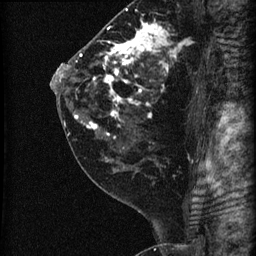
Breast MRI (dynamic contrast-enhanced), one sagittal slice. Position 38 of 60 along the scan axis. Dynamic contrast-enhanced series, image 2 of 3 at this slice position (ordered by acquisition). 1.5 T. TE 4.2 ms, TR 22.7 ms. 1.8 mm slice thickness. 256 × 256 image matrix. Patient: female, 45 years. Case-level facts recorded for this patient, not image findings: setting: breast cancer imaged before/during neoadjuvant chemotherapy; receptor status: HR-positive, HER2-negative.
Annotated regions visible in this slice (semi-automatically segmented with operator editing):
- analysis volume of interest (the breast-tissue region the enhancement analysis was run in; not a lesion): bounding box (x1, y1, x2, y2) in pixels: (74, 11, 205, 140)
- tumour enhancement mask (voxels above the 90 % enhancement threshold inside the analysis volume of interest): (75, 22, 183, 136)